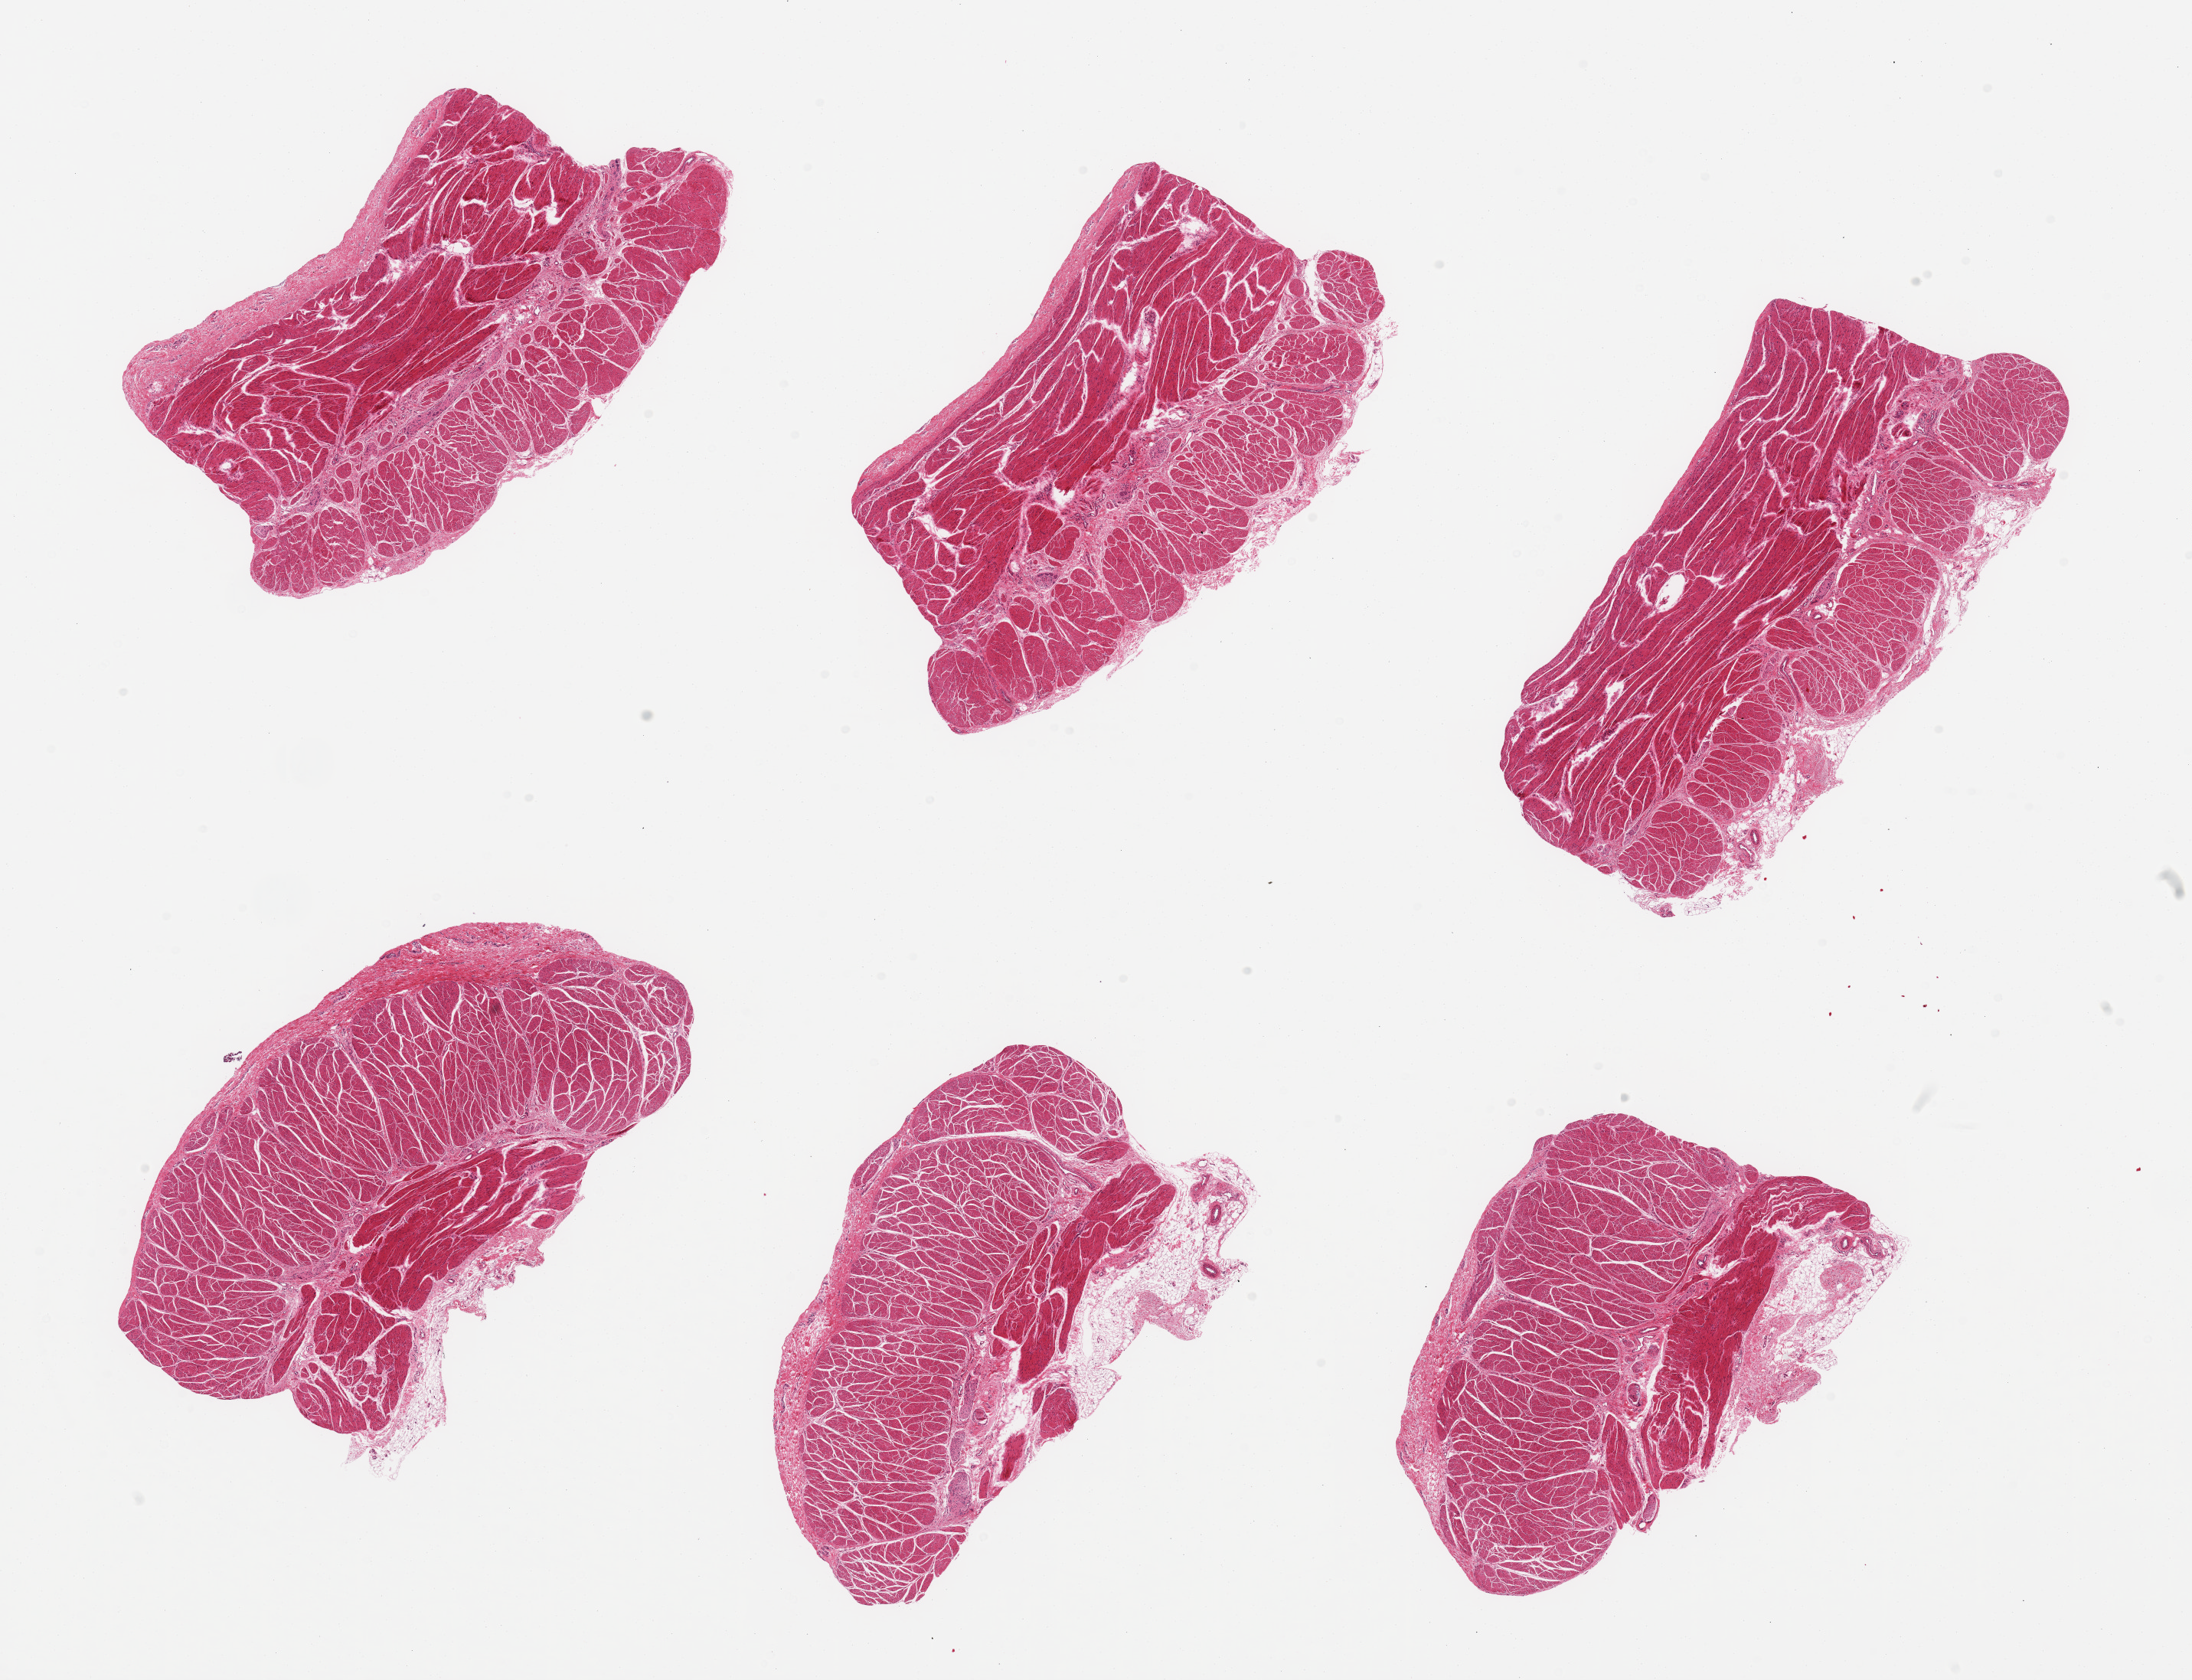
Haematoxylin and eosin whole-slide image, brightfield — shown as a low-resolution overview of the whole scanned area (about 22.6 x 17.4 mm, from a 20x scan). PAXgene-fixed paraffin-embedded (PFPE) section. Sampled site (target tissue): gastroesophageal junction. Tissue donor sample. Donor sex: female.
Reviewer comment on this tissue sample: 6 pieces; 4 pieces well dissected muscularis, 2 have 20% fibrofatty adventitia with prominent nerves.